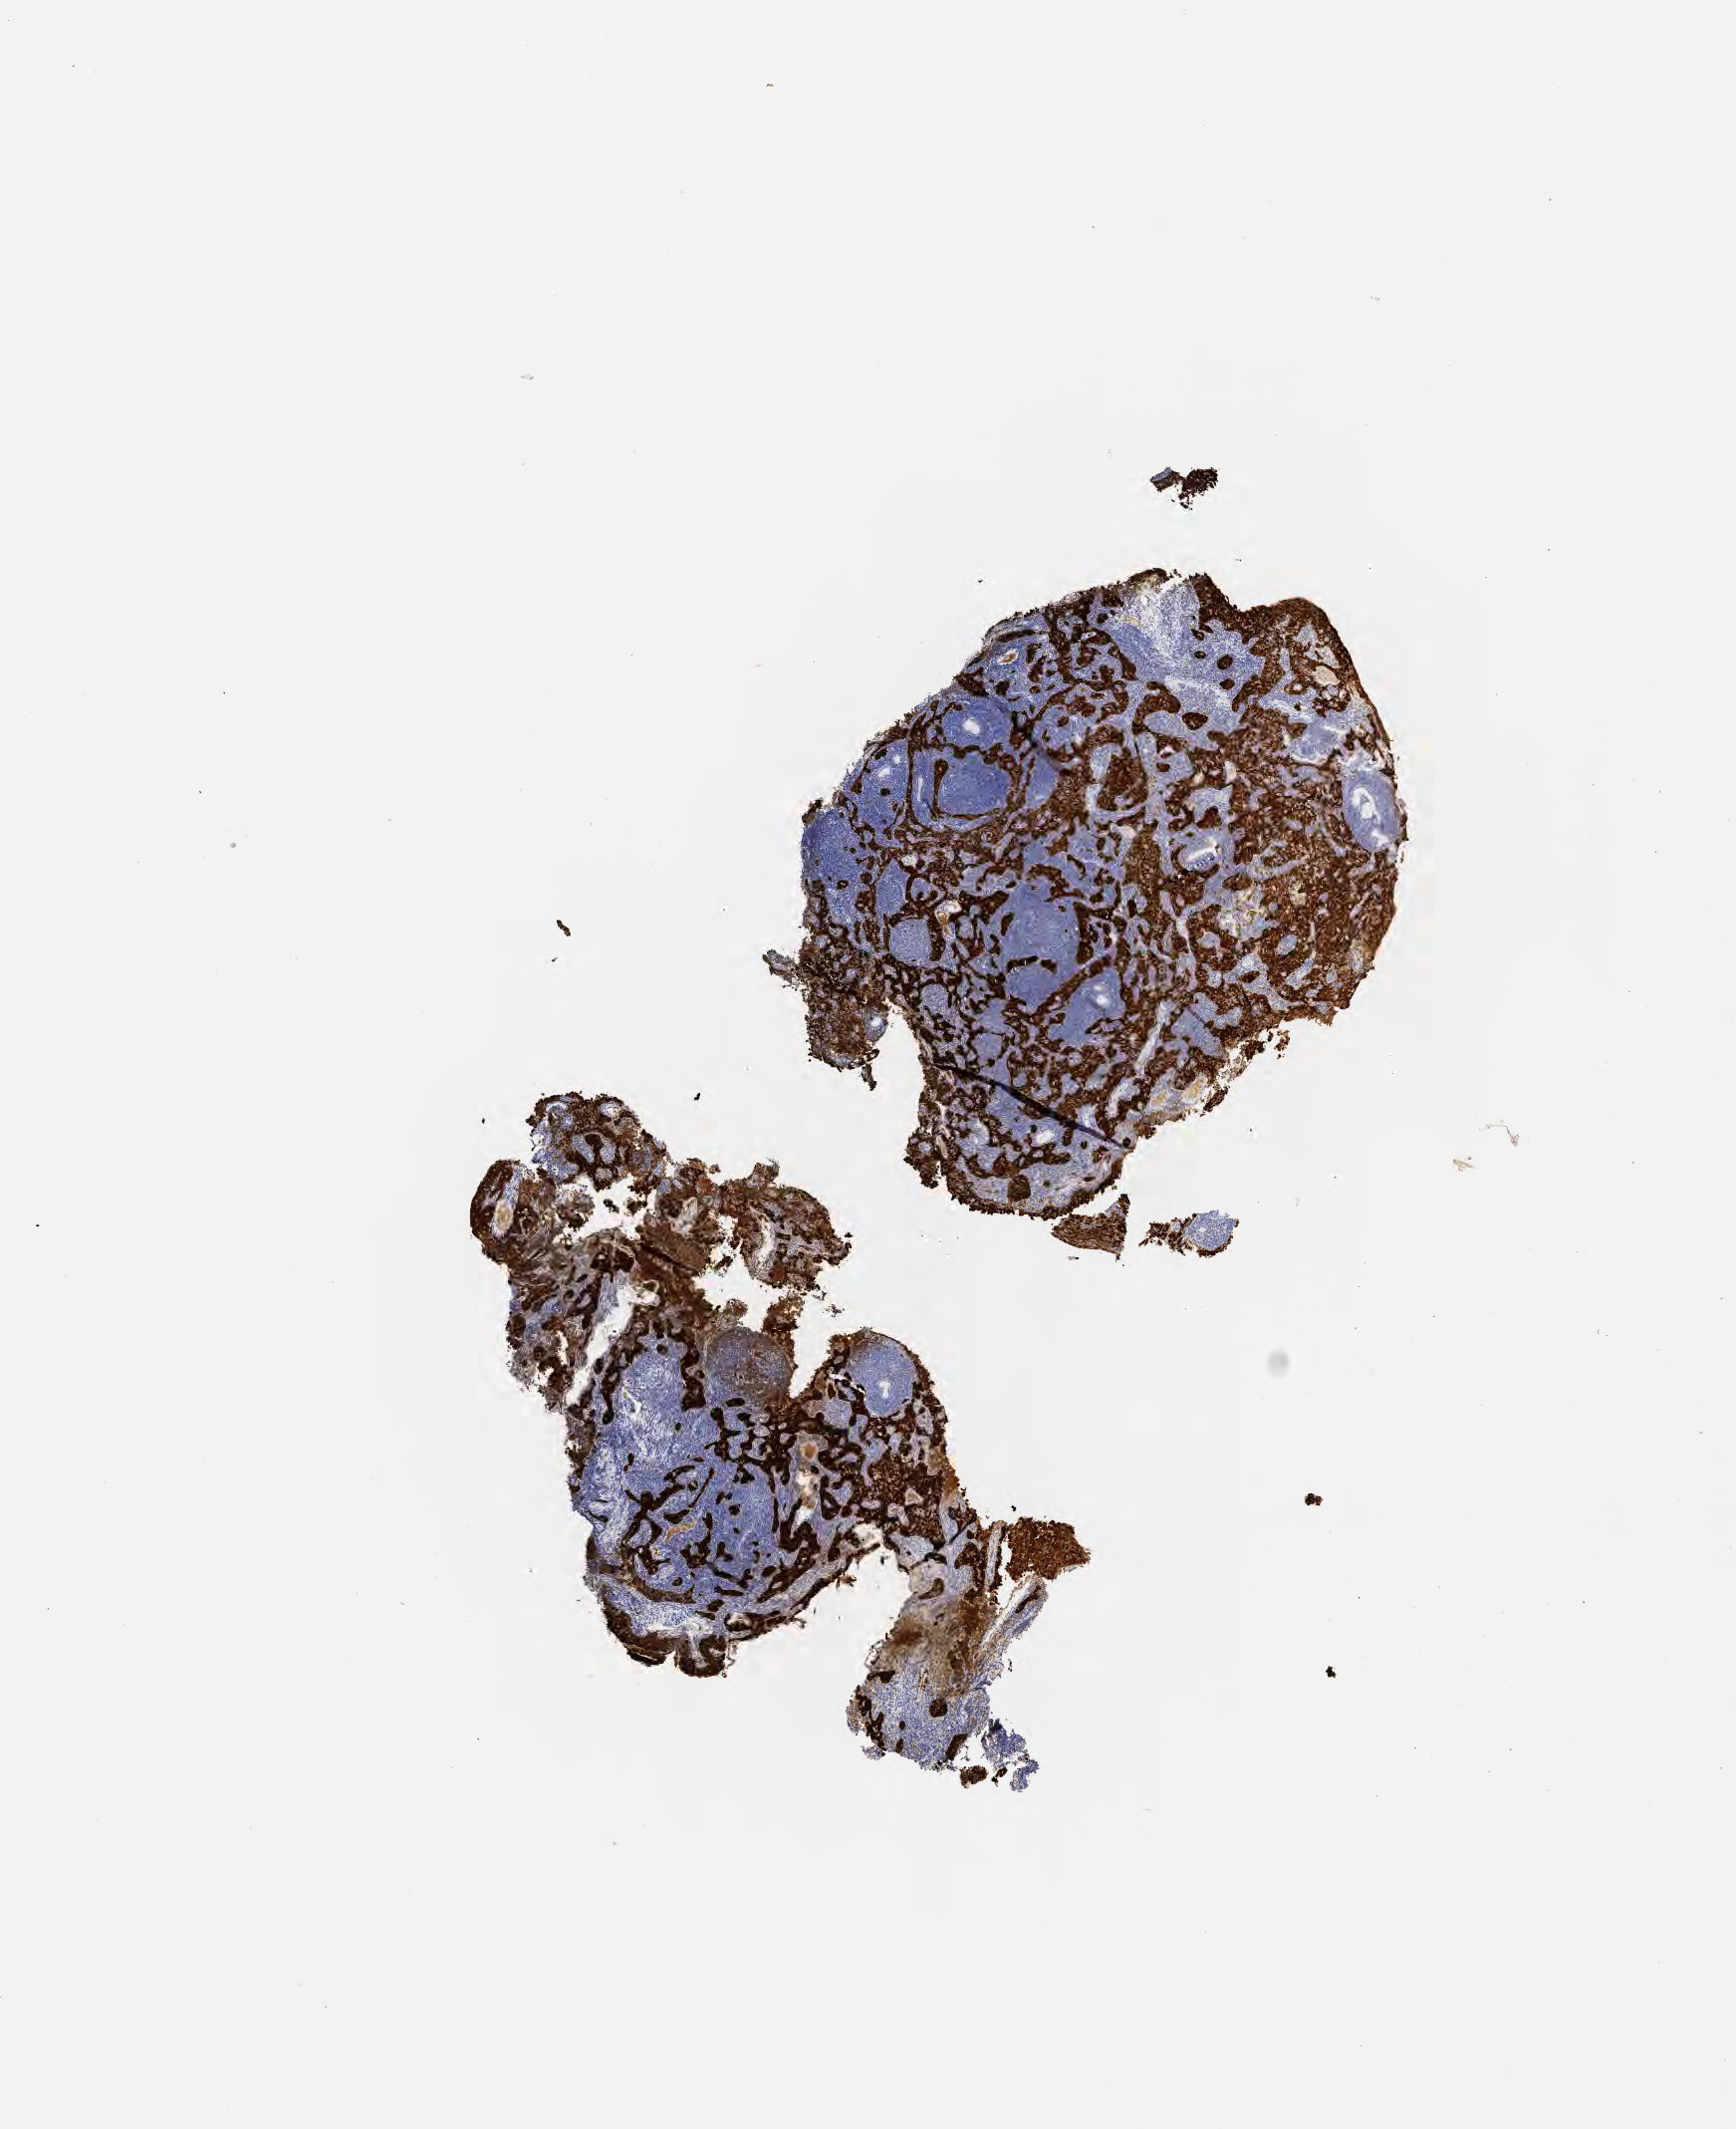
Immunohistochemistry (IHC) whole-slide image stained for p16 (p16INK4a) — shown as a low-resolution overview of the whole scanned area (about 7.0 x 8.6 mm); tumor tissue; site: cervix. Patient female; aged 44.
Diagnosis: Squamous cell carcinoma, large cell, nonkeratinizing, NOS.